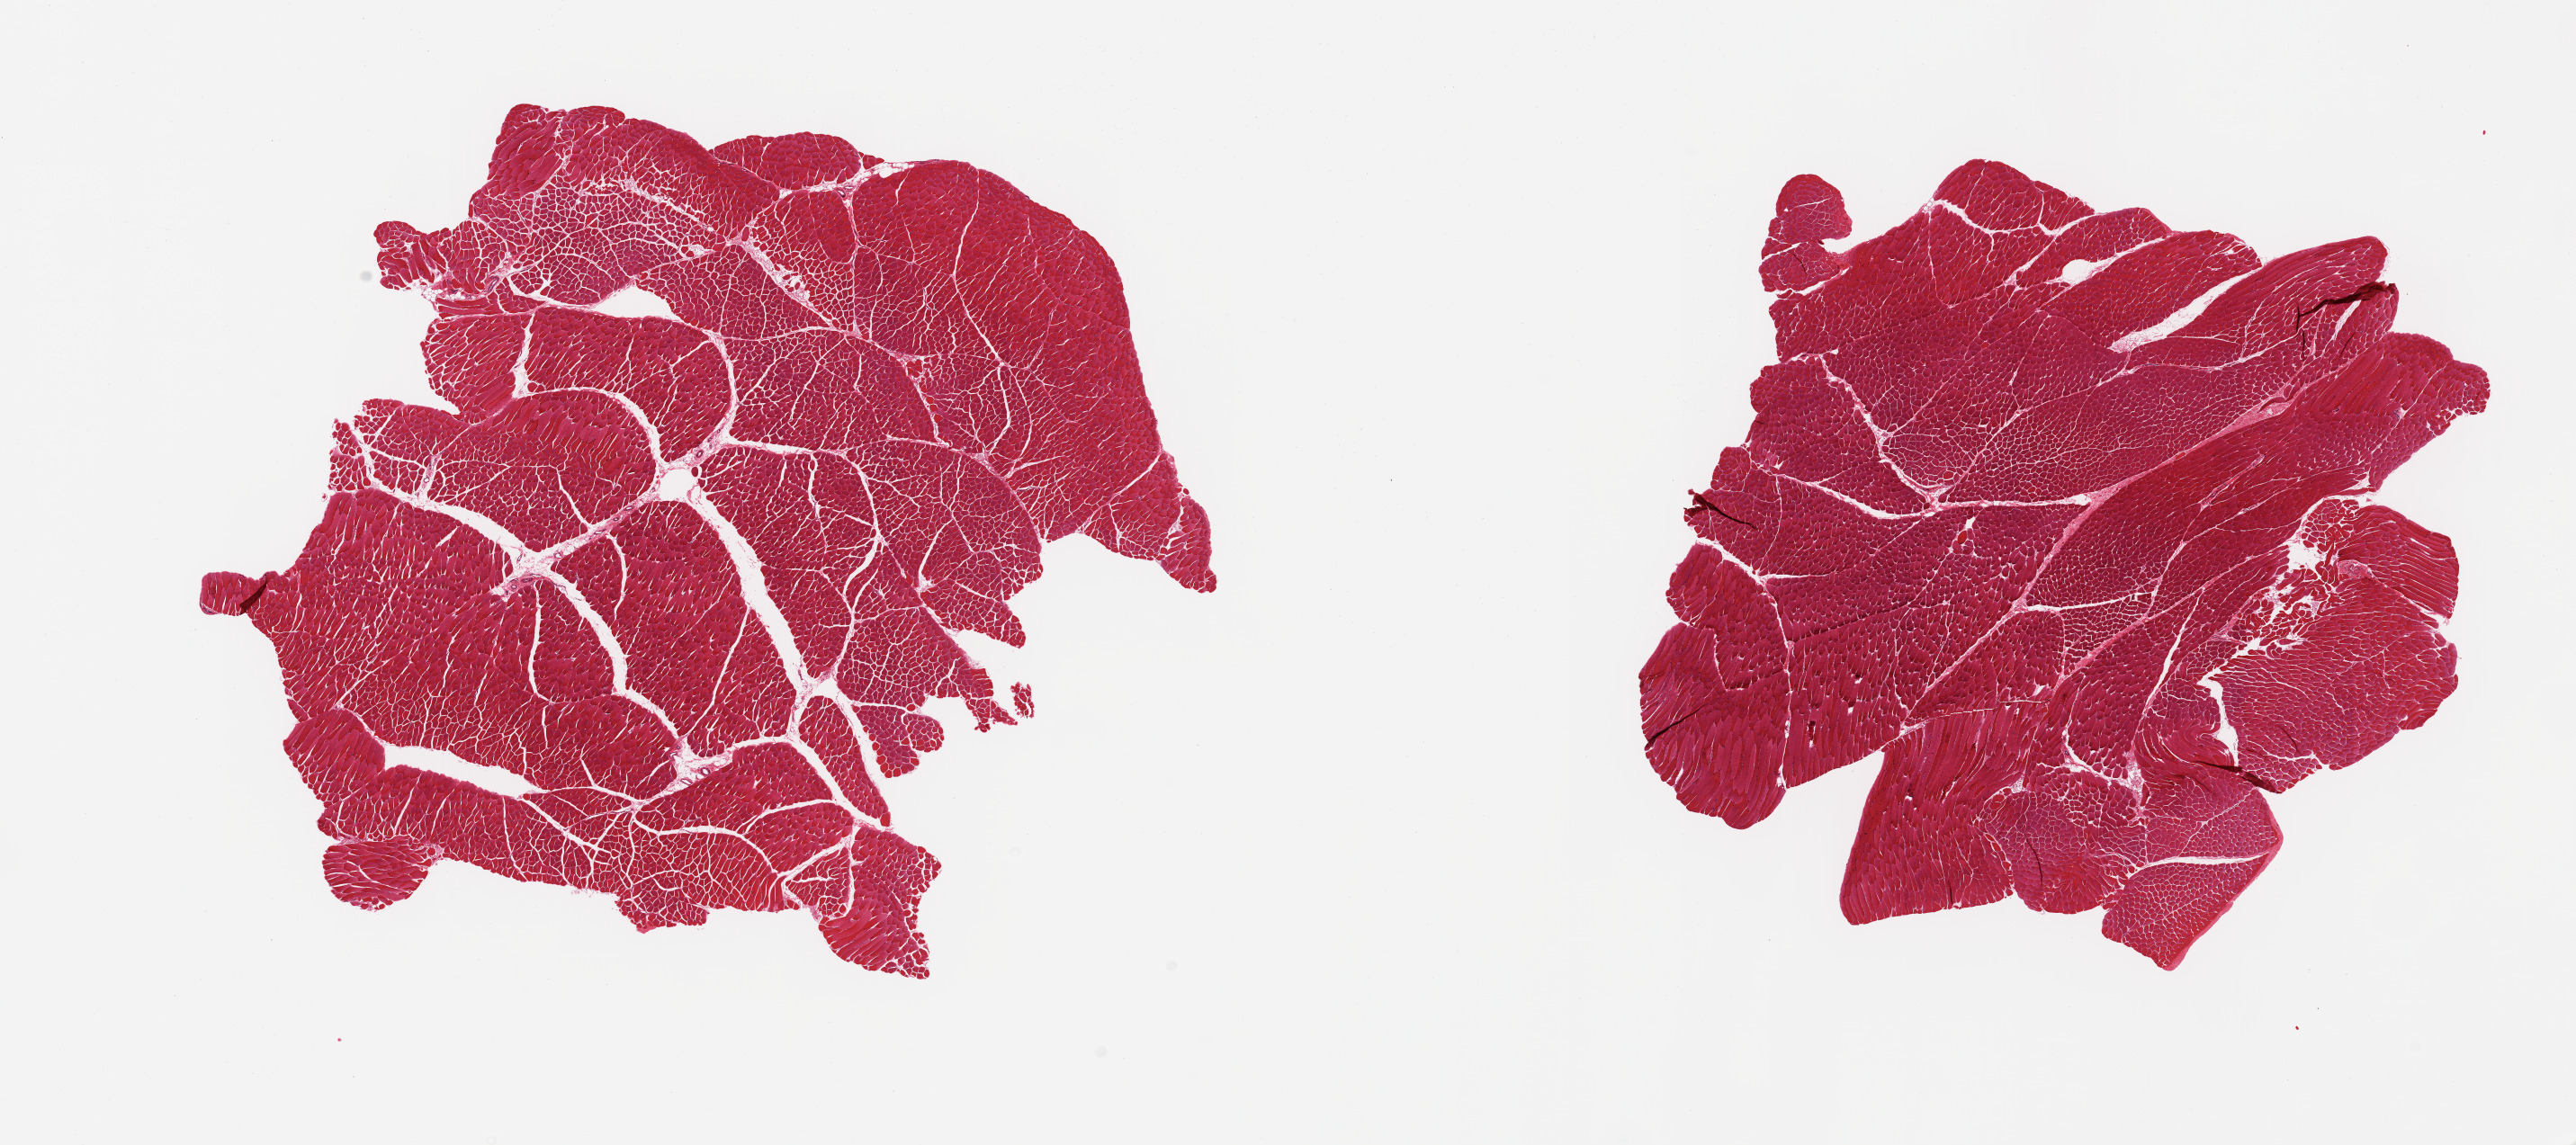
Whole-slide image, H&E stain, shown as a low-resolution overview of the whole scanned area (about 22.6 x 10.1 mm); PAXgene-fixed paraffin-embedded (PFPE) section; target tissue: skeletal muscle; tissue donor sample. Donor: male.
- reviewer comment on this tissue sample: 2 pieces; minimal interstitial fat